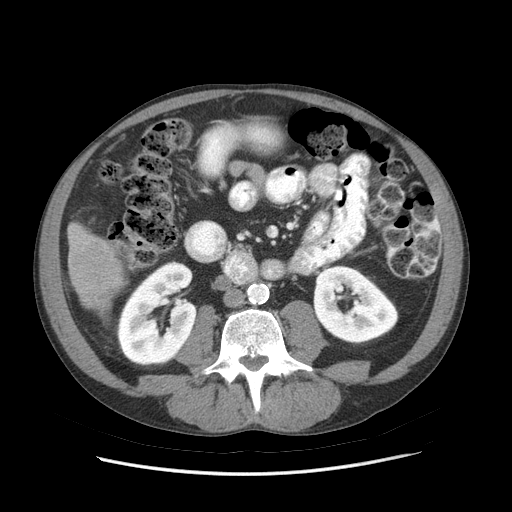
Contrast-enhanced abdominal CT (liver protocol), one axial slice; slice 15 of 89 in the series (ordered by position); reconstruction kernel STANDARD; soft-tissue window (W 400 / L 40 HU); 512 × 512 image matrix, field of view 380 × 380 mm. From the clinical record (not read from this slice): diagnosis: hepatocellular carcinoma (patient treated with transarterial chemoembolisation; whether this scan precedes or follows treatment is not stated here); TNM stage (as recorded): Stage-IIIB; Child-Pugh class: A; tumour differentiation: moderately differentiated.
Annotated regions visible in this slice (semi-automatic segmentation, software-assisted and operator-edited):
- liver parenchyma outside the tumour (the mass and vessels are separate outlines, so this box may not span the whole liver): bounding box <68,222,124,311> (left, top, right, bottom; pixels)